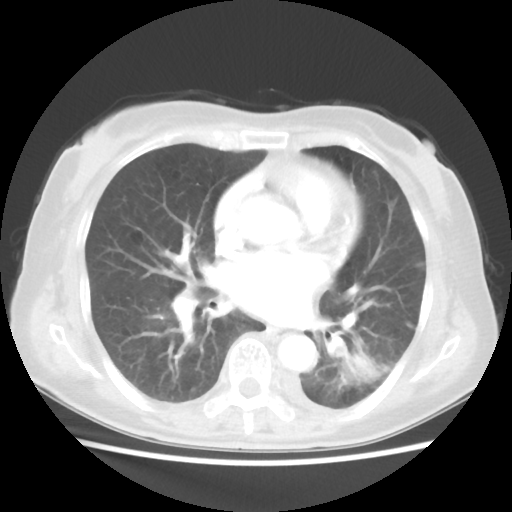
Chest CT, one axial slice; position 17 of 40 along the scan axis; reconstruction kernel STANDARD; lung window (W 1500 / L -600 HU); 512 × 512 image matrix, field of view 341 × 341 mm. Female patient, age 69 years. Case-level facts recorded for this patient, not image findings: clinical TNM (as recorded): T1c N0 M0.
Structures marked on this image (bounding box drawn by a radiologist):
- lung tumour (recorded histology: adenocarcinoma): box from (x=338, y=346) to (x=376, y=386) px